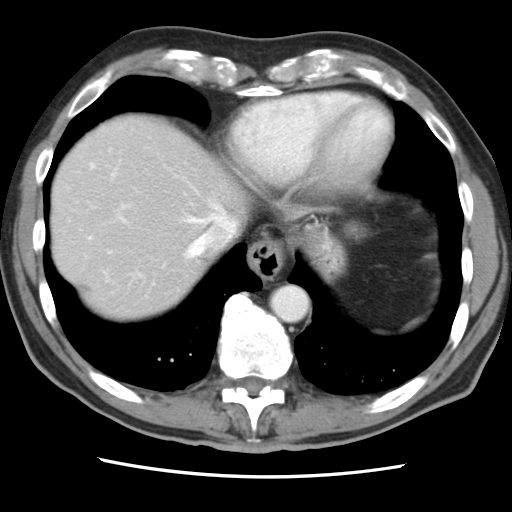
Contrast-enhanced abdominal CT, one axial slice; slice 73 of 83 in the series (ordered by position); 120 kVp; intravenous contrast given; soft-tissue window (W 400 / L 40 HU); 5 mm slice thickness; 512 × 512 image matrix, field of view 321 × 321 mm. Male patient, age 69 years. From the clinical record (not read from this slice): diagnosis: colorectal cancer liver metastases, imaged before liver resection; multiple liver metastases: yes; largest metastasis: 3.5 cm; chemotherapy before resection: yes.
Structures marked on this image (expert manual segmentation):
- hepatic veins: bounding box <89,163,236,276> (left, top, right, bottom; pixels)
- liver: <52,113,246,322>
- planned liver remnant (the part of the liver to remain after resection): <52,152,211,322>
- portal vein (with intrahepatic branches): <112,171,126,223>